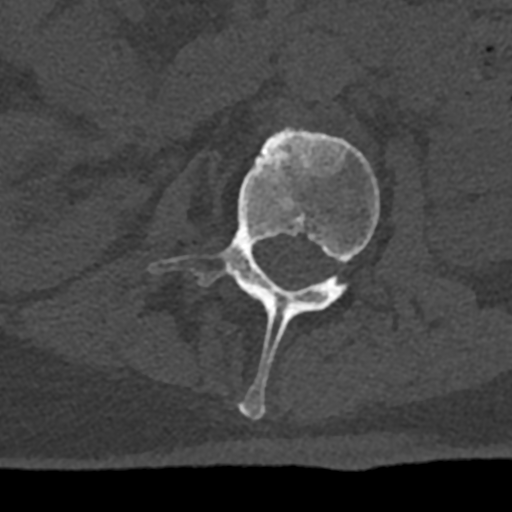
CT including the spine, one axial slice; position 375 of 797 along the scan axis; 120 kVp; bone window (W 1800 / L 400 HU); 0.5 mm slice thickness; 512 × 512 image matrix, field of view 160 × 160 mm. Male patient, age 74 years. From the clinical record (not read from this slice): primary cancer: renal; vertebrae with lytic lesions (as recorded): T10, L1, L2, L3, L4, L5.
Outlined on this slice (semi-automatic segmentation, software-assisted and operator-edited):
- L2 vertebra: bounding box (x1, y1, x2, y2) in pixels: (148, 128, 380, 419)